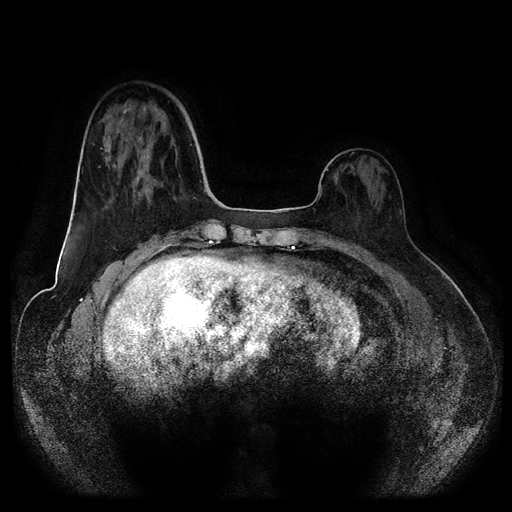
Breast MRI (dynamic contrast-enhanced, multi-phase), one axial slice; position 32 of 116 along the scan axis; dynamic contrast-enhanced series, time point 2 of 5 at this slice position (early post-contrast); 1.5 T; TE 2.6 ms, TR 5.2 ms; 2 mm slice thickness; 512 × 512 image matrix, field of view 380 × 380 mm. Female patient, age 50 years.
Outlined on this slice (semi-automatic segmentation, software-assisted and operator-edited):
- breast lesion (labelled benign in the annotation): bounding box <136,132,154,186> (left, top, right, bottom; pixels)